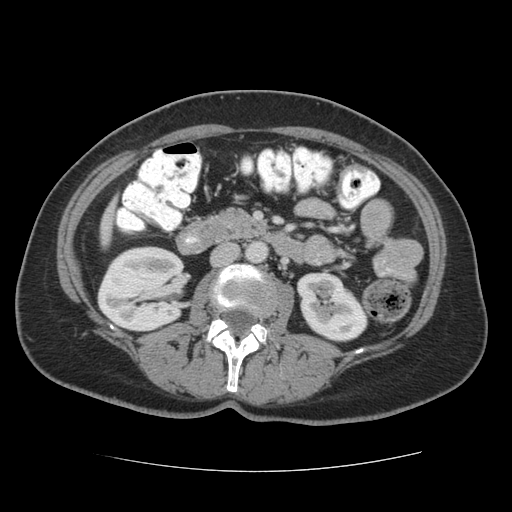
Contrast-enhanced abdominal CT (liver protocol), one axial slice. Position 10 of 75 along the scan axis. 140 kVp. Soft-tissue window (W 400 / L 40 HU). 2.5 mm slice thickness. 512 × 512 image matrix, field of view 360 × 360 mm. Case-level facts recorded for this patient, not image findings: diagnosis: hepatocellular carcinoma (patient treated with transarterial chemoembolisation; whether this scan precedes or follows treatment is not stated here); TNM stage (as recorded): Stage-I; Child-Pugh class: A; tumour differentiation: moderately differentiated; tumour nodularity: uninodular.
Structures marked on this image (semi-automatically segmented with operator editing):
- liver parenchyma outside the tumour (the mass and vessels are separate outlines, so this box may not span the whole liver): bounding box [x1, y1, x2, y2] px = [100, 216, 110, 246]